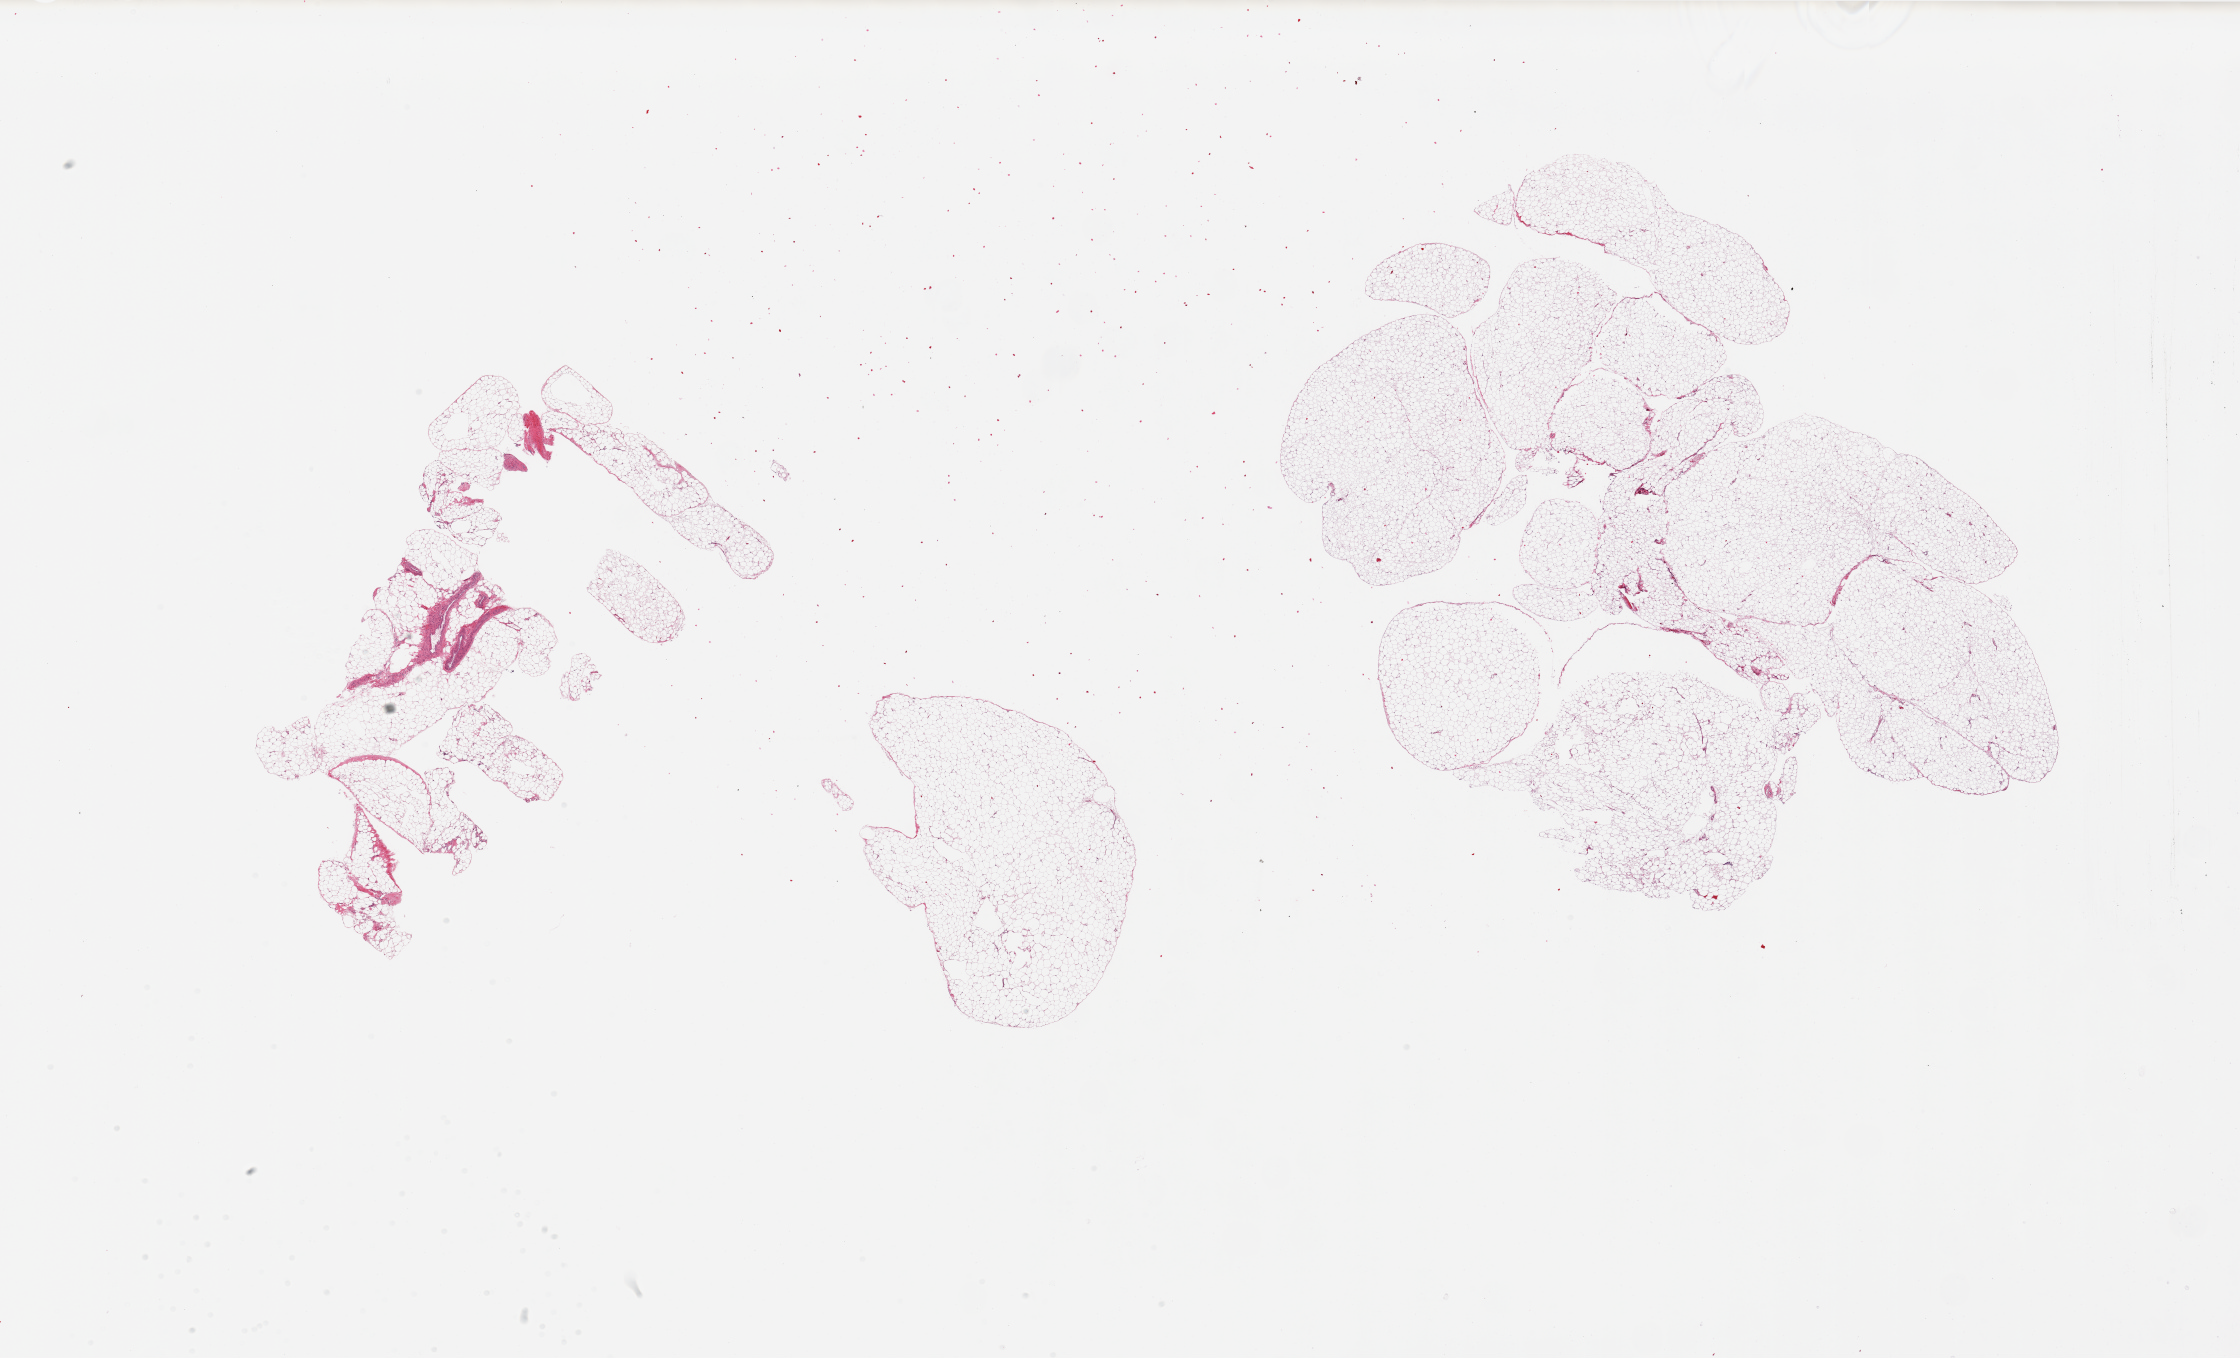
Whole-slide image, haematoxylin and eosin stain — a low-resolution overview of the entire scanned area, about 35.4 x 21.5 mm. PAXgene-fixed paraffin-embedded (PFPE) section. Sampled site (target tissue): omentum. Tissue donor sample. Donor: male.
* pathologist's review note for this sample: 2 pieces, trace fascia/vascular elements